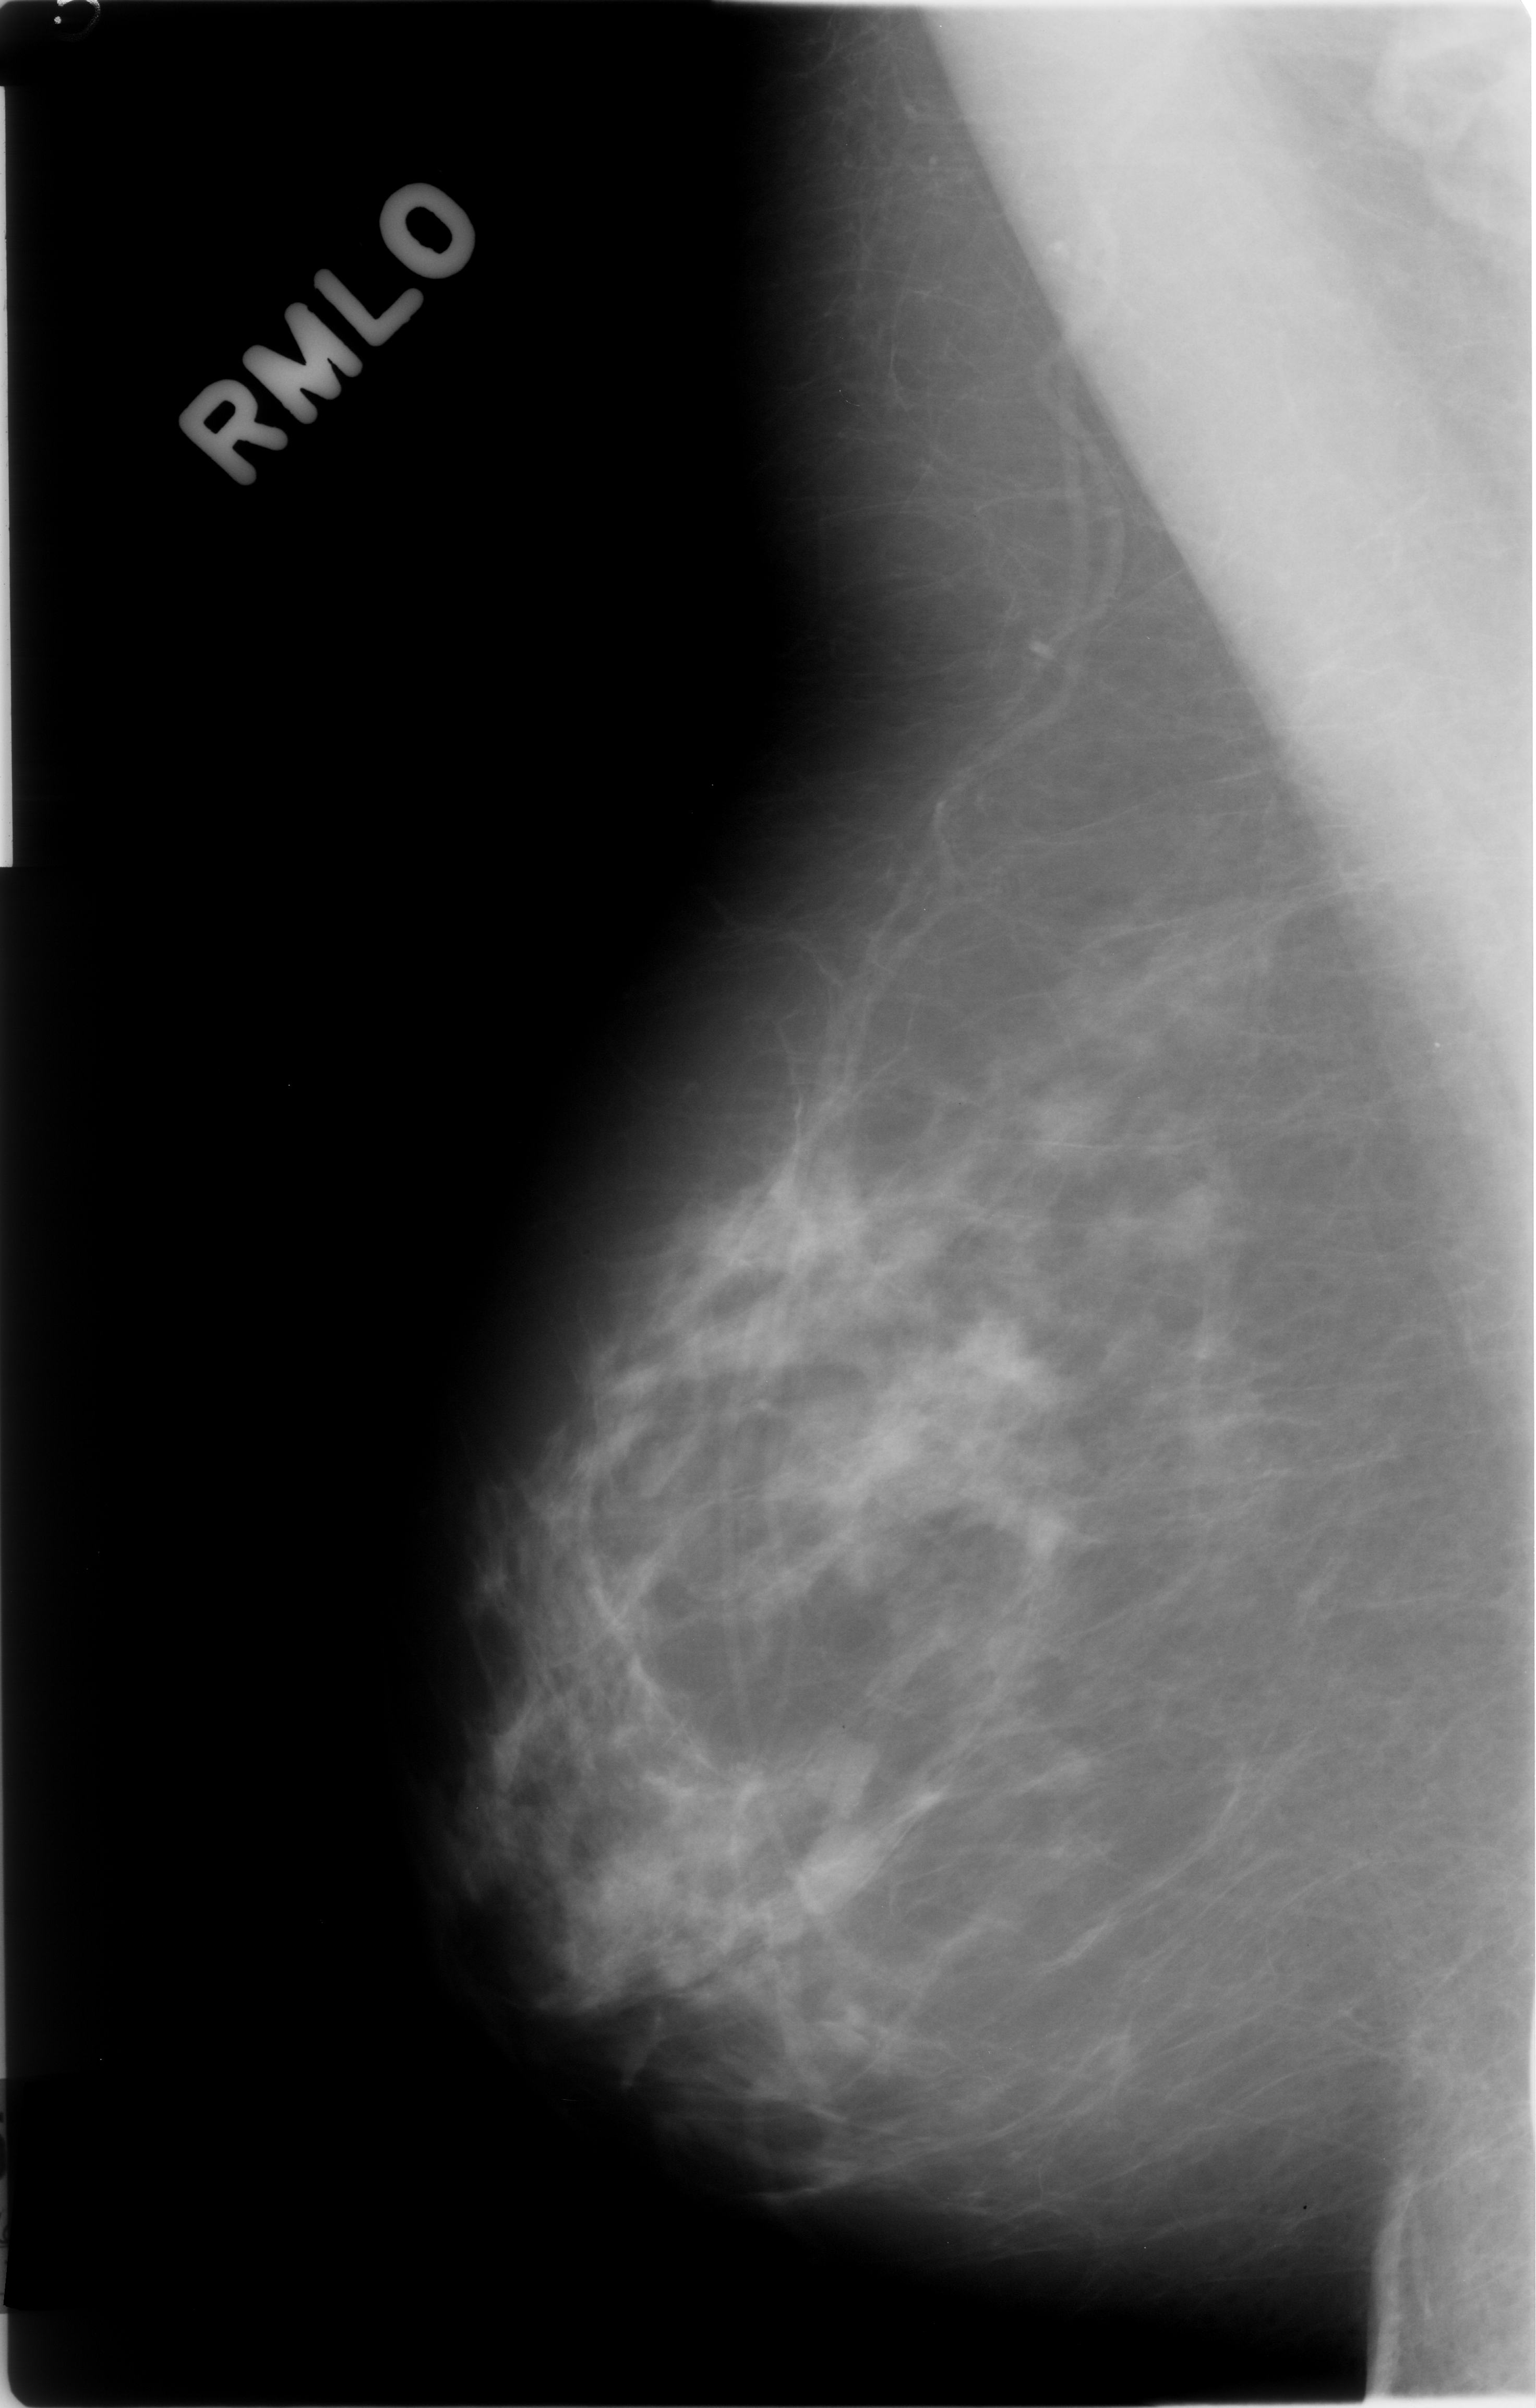
Scanned film-screen mammogram, right breast, mediolateral oblique (MLO) view, BI-RADS breast density category 2 (scale 1–4).
- Radiologist-marked abnormalities on this image: mass, shape oval, margins circumscribed; BI-RADS assessment category 3; pathology result (as recorded, not read from the image): benign.